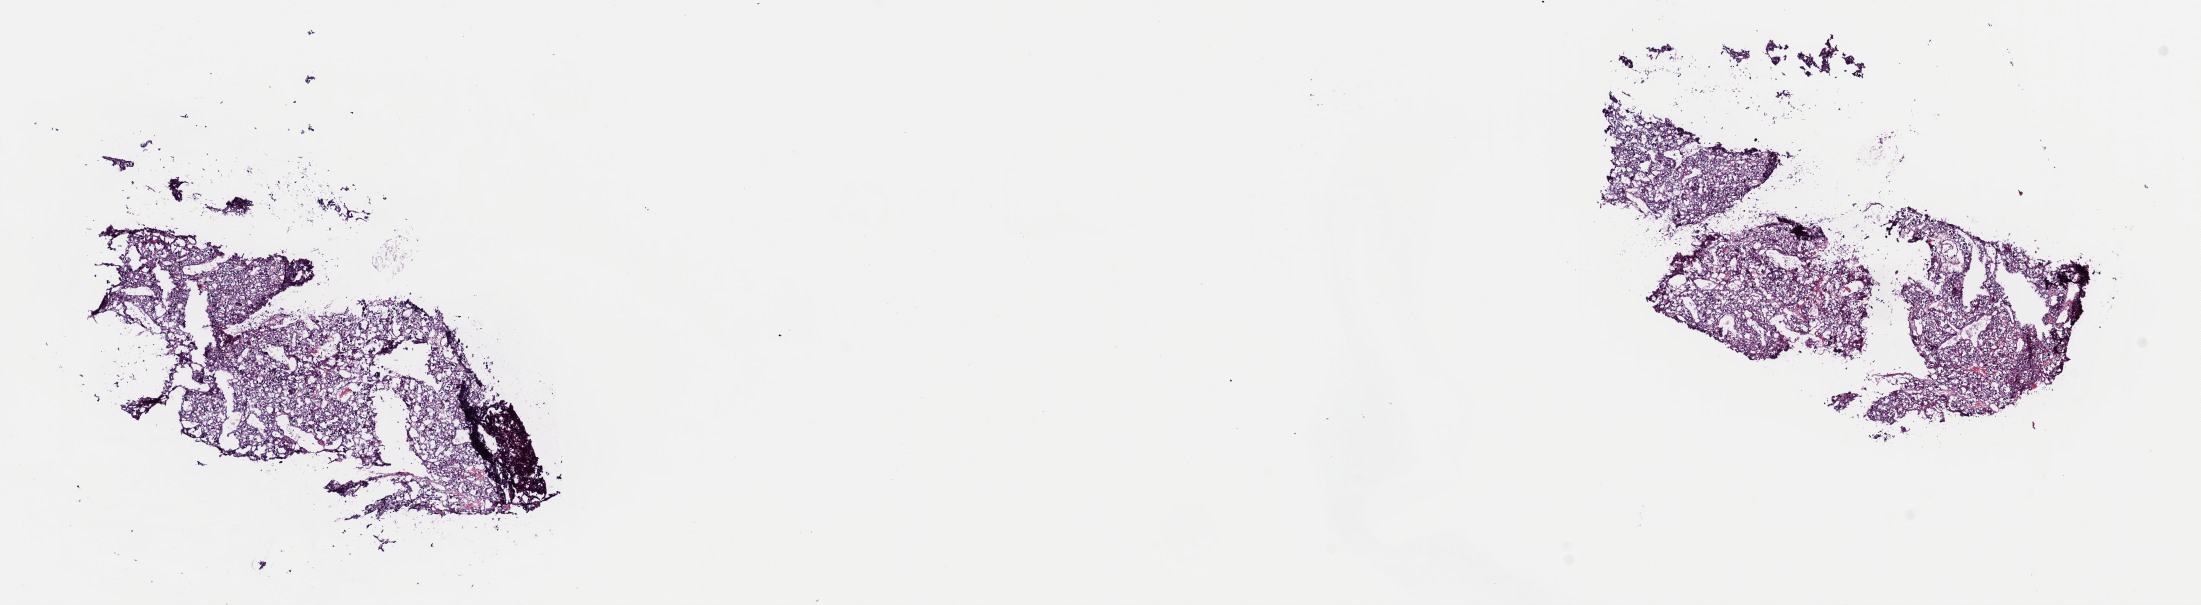
Digitized H&E tissue section (whole slide), low-resolution overview of the scanned area, about 17.4 x 4.8 mm (from a 40x scan), frozen section from the top of the tissue portion, adrenal gland, primary tumour sample. Male, age 32 years at initial diagnosis. Pathologist review of this section (percent, as recorded): tumour cells 90%, tumour nuclei 100%, normal cells 0%, stromal cells 10%, necrosis 0%. Infiltration values recorded for this section: lymphocyte infiltration 3%, monocyte infiltration 0%, neutrophil infiltration 0%.
Histologic diagnosis: Pheochromocytoma, NOS. Laterality: left.